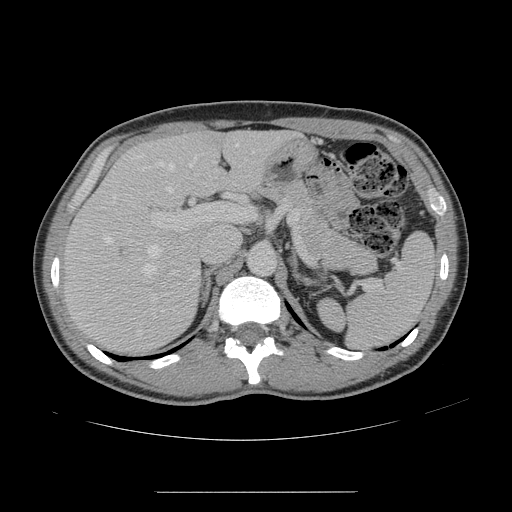
Contrast-enhanced abdominal CT, one axial slice. Slice 94 of 178 in the series (ordered by position). 120 kVp. Intravenous contrast given. Soft-tissue window (W 400 / L 40 HU). 2.5 mm slice thickness. 512 × 512 image matrix, field of view 401 × 401 mm. Male patient, age 53 years. From the clinical record (not read from this slice): diagnosis: colorectal cancer liver metastases, imaged before liver resection; multiple liver metastases: yes; largest metastasis: 2.4 cm; disease in both lobes: no.
Annotated regions visible in this slice (manually delineated by an expert):
- hepatic veins: box from (x=104, y=143) to (x=238, y=277) px
- liver: (x=66, y=131)–(x=289, y=351)
- planned liver remnant (the part of the liver to remain after resection): (x=148, y=131)–(x=289, y=193)
- portal vein (with intrahepatic branches): (x=151, y=204)–(x=255, y=274)